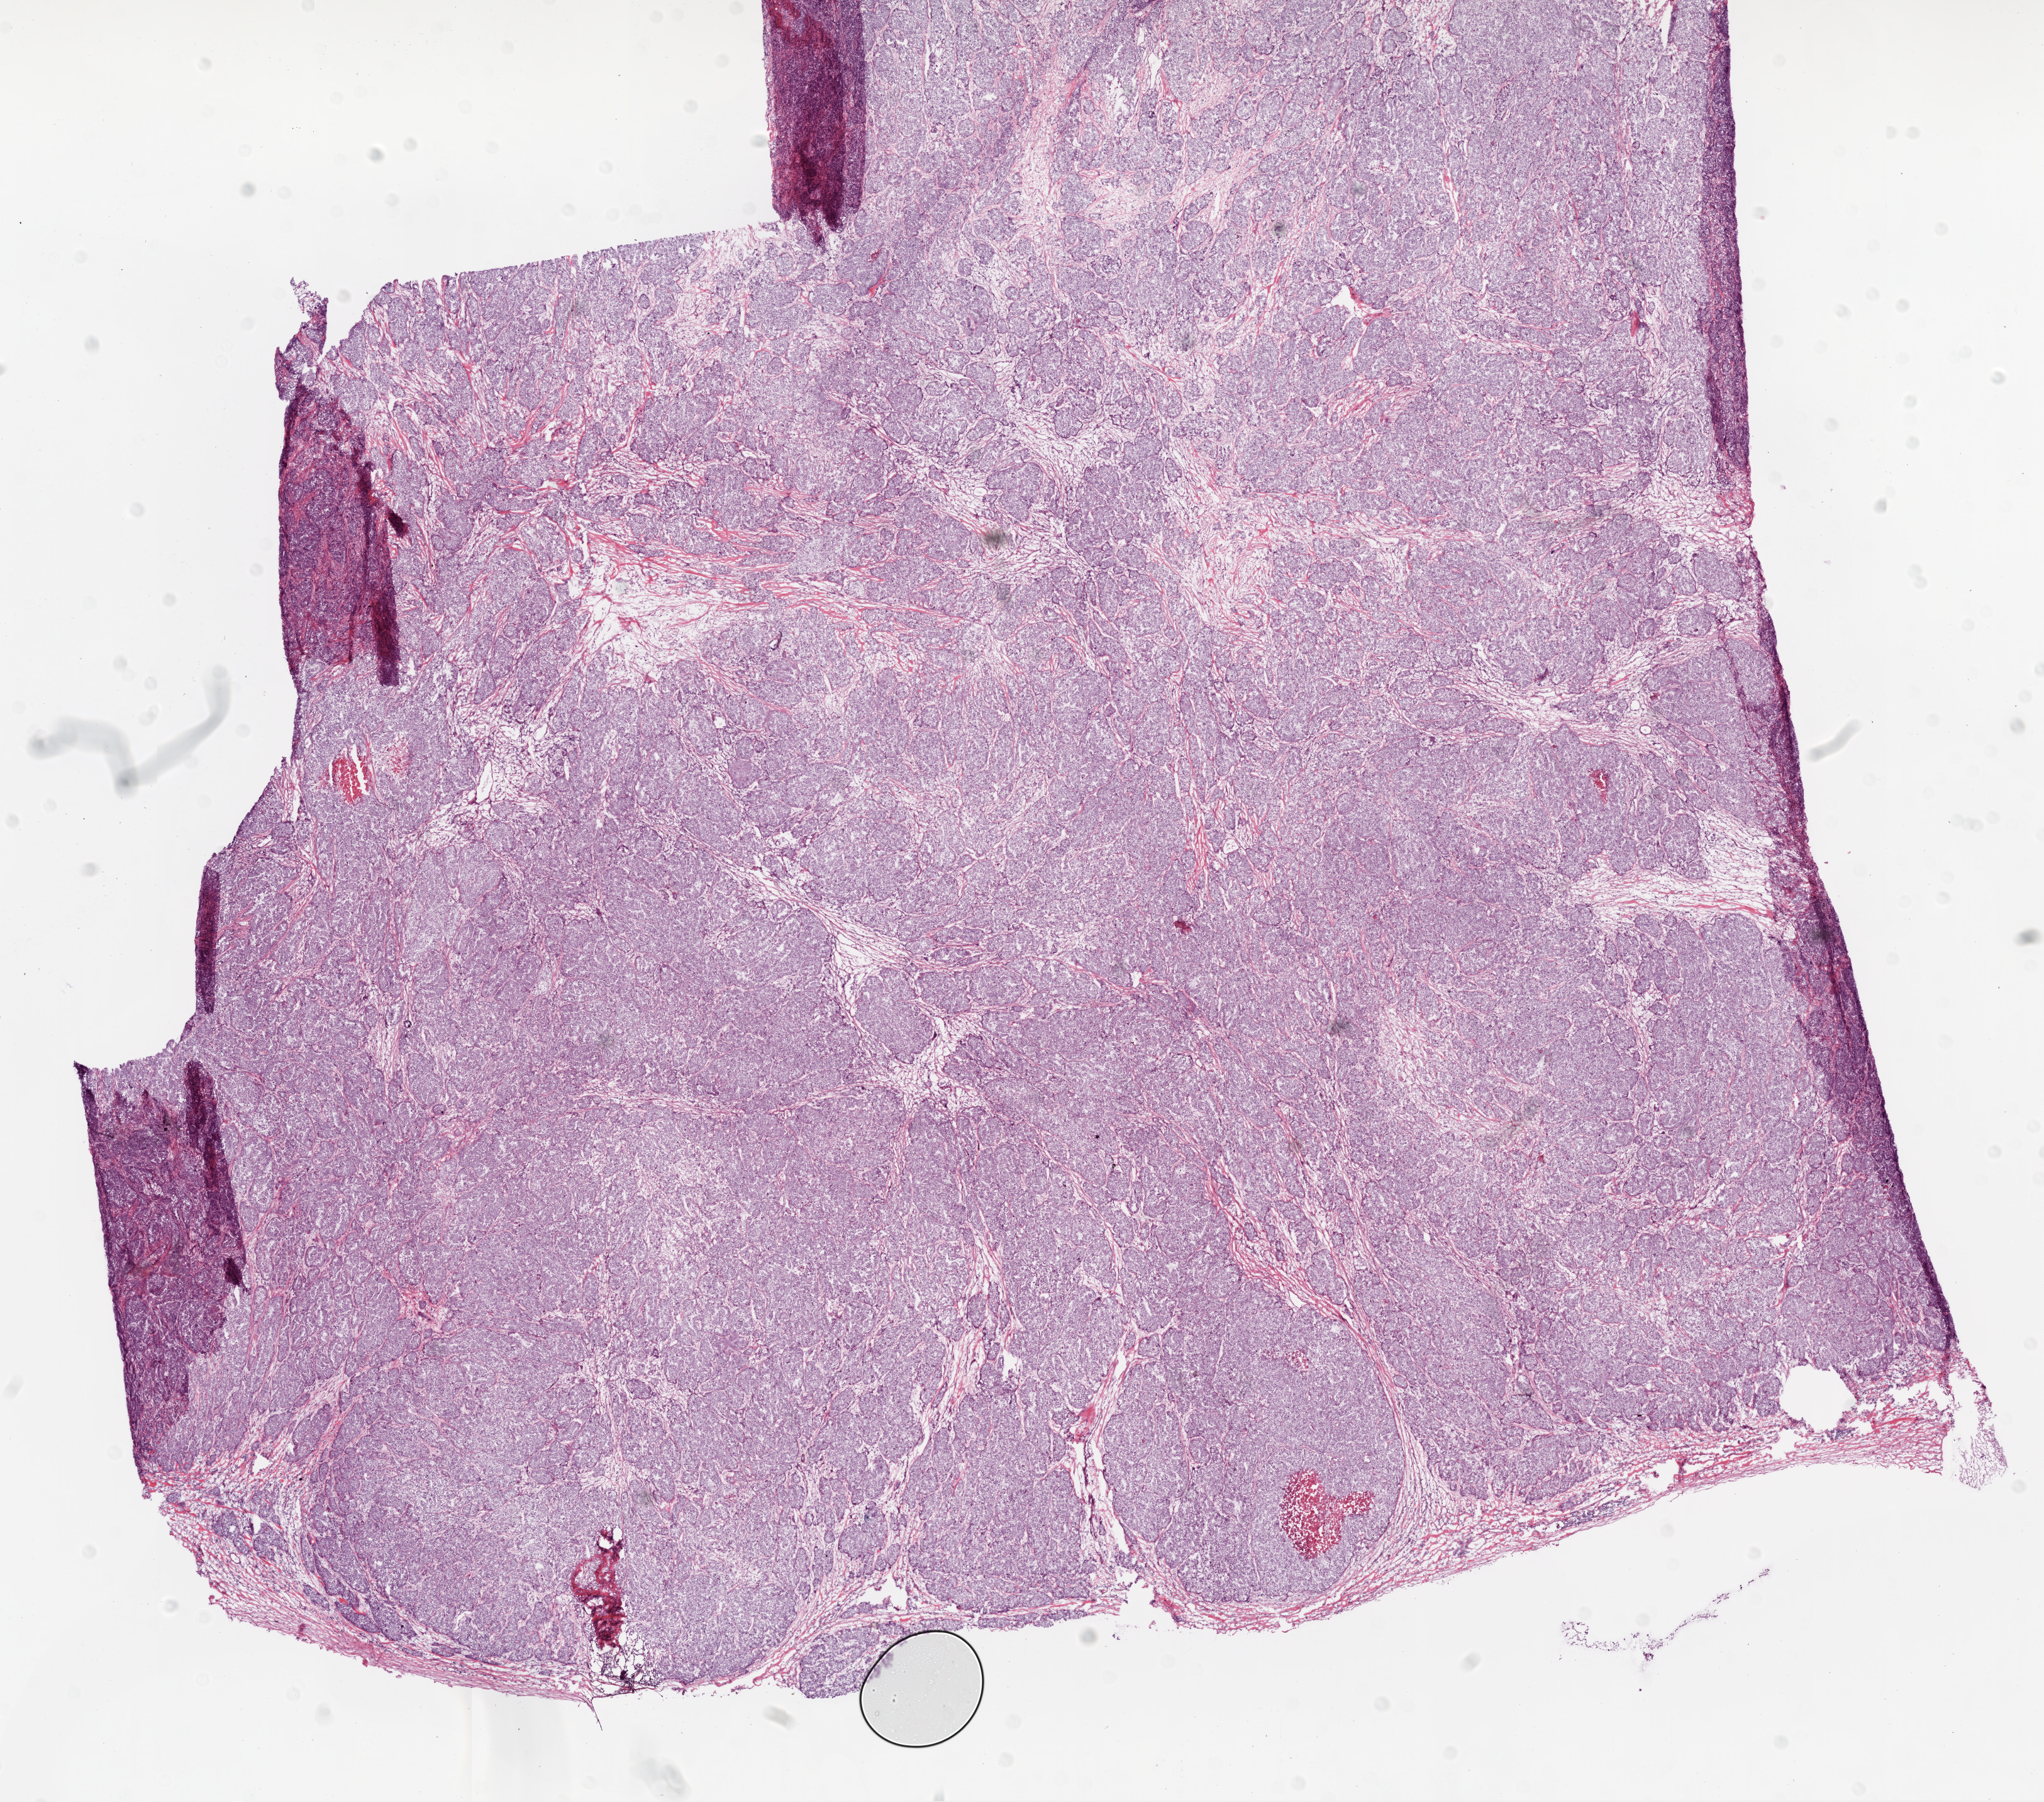
Digitized H&E tissue section (whole slide) — whole scanned area (about 13.0 x 11.5 mm) shown as a low-resolution overview, frozen section from the bottom of the tissue portion, ovary, primary tumour sample. Female patient; age at initial diagnosis 47 years. Histologic grade: G3 (poorly differentiated). Slide review estimates, as recorded: tumour cells 95%, tumour nuclei 90%, normal cells 0%, stromal cells 0%, necrosis 5%.
Diagnosis: Serous cystadenocarcinoma, NOS. FIGO stage: IIIC.